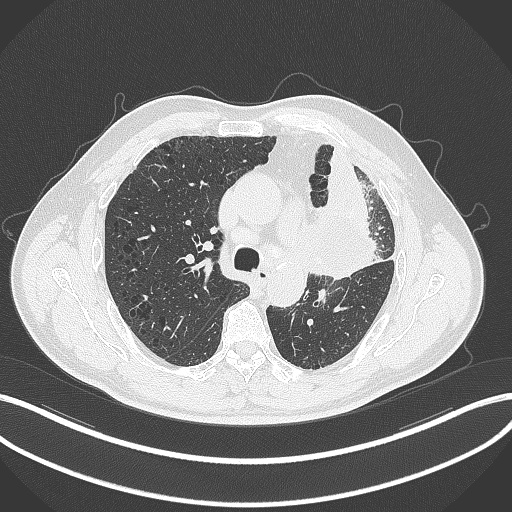
Chest CT, one axial slice. Position 205 of 297 along the scan axis. Reconstruction kernel B70f. 120 kVp. Lung window (W 1500 / L -600 HU). 1 mm slice thickness. 512 × 512 image matrix, field of view 400 × 400 mm. Patient: male, 68 years. Case-level facts recorded for this patient, not image findings: clinical TNM (as recorded): T3 N3 M1.
Structures marked on this image (bounding box drawn by a radiologist):
- lung tumour (recorded histology: adenocarcinoma): bounding box <302,196,385,282> (left, top, right, bottom; pixels)